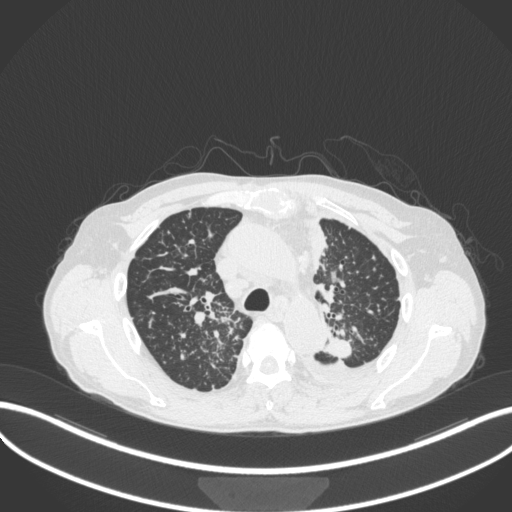
Chest CT, one axial slice. Position 255 of 319 along the scan axis. 120 kVp. Lung window (W 1500 / L -600 HU). 512 × 512 image matrix, field of view 400 × 400 mm. Patient: male, 58 years. Case-level facts recorded for this patient, not image findings: clinical TNM (as recorded): T1c N3 M1.
Structures marked on this image (rectangle marked by the reading radiologist):
- lung tumour (recorded histology: adenocarcinoma): box from (x=315, y=332) to (x=358, y=360) px